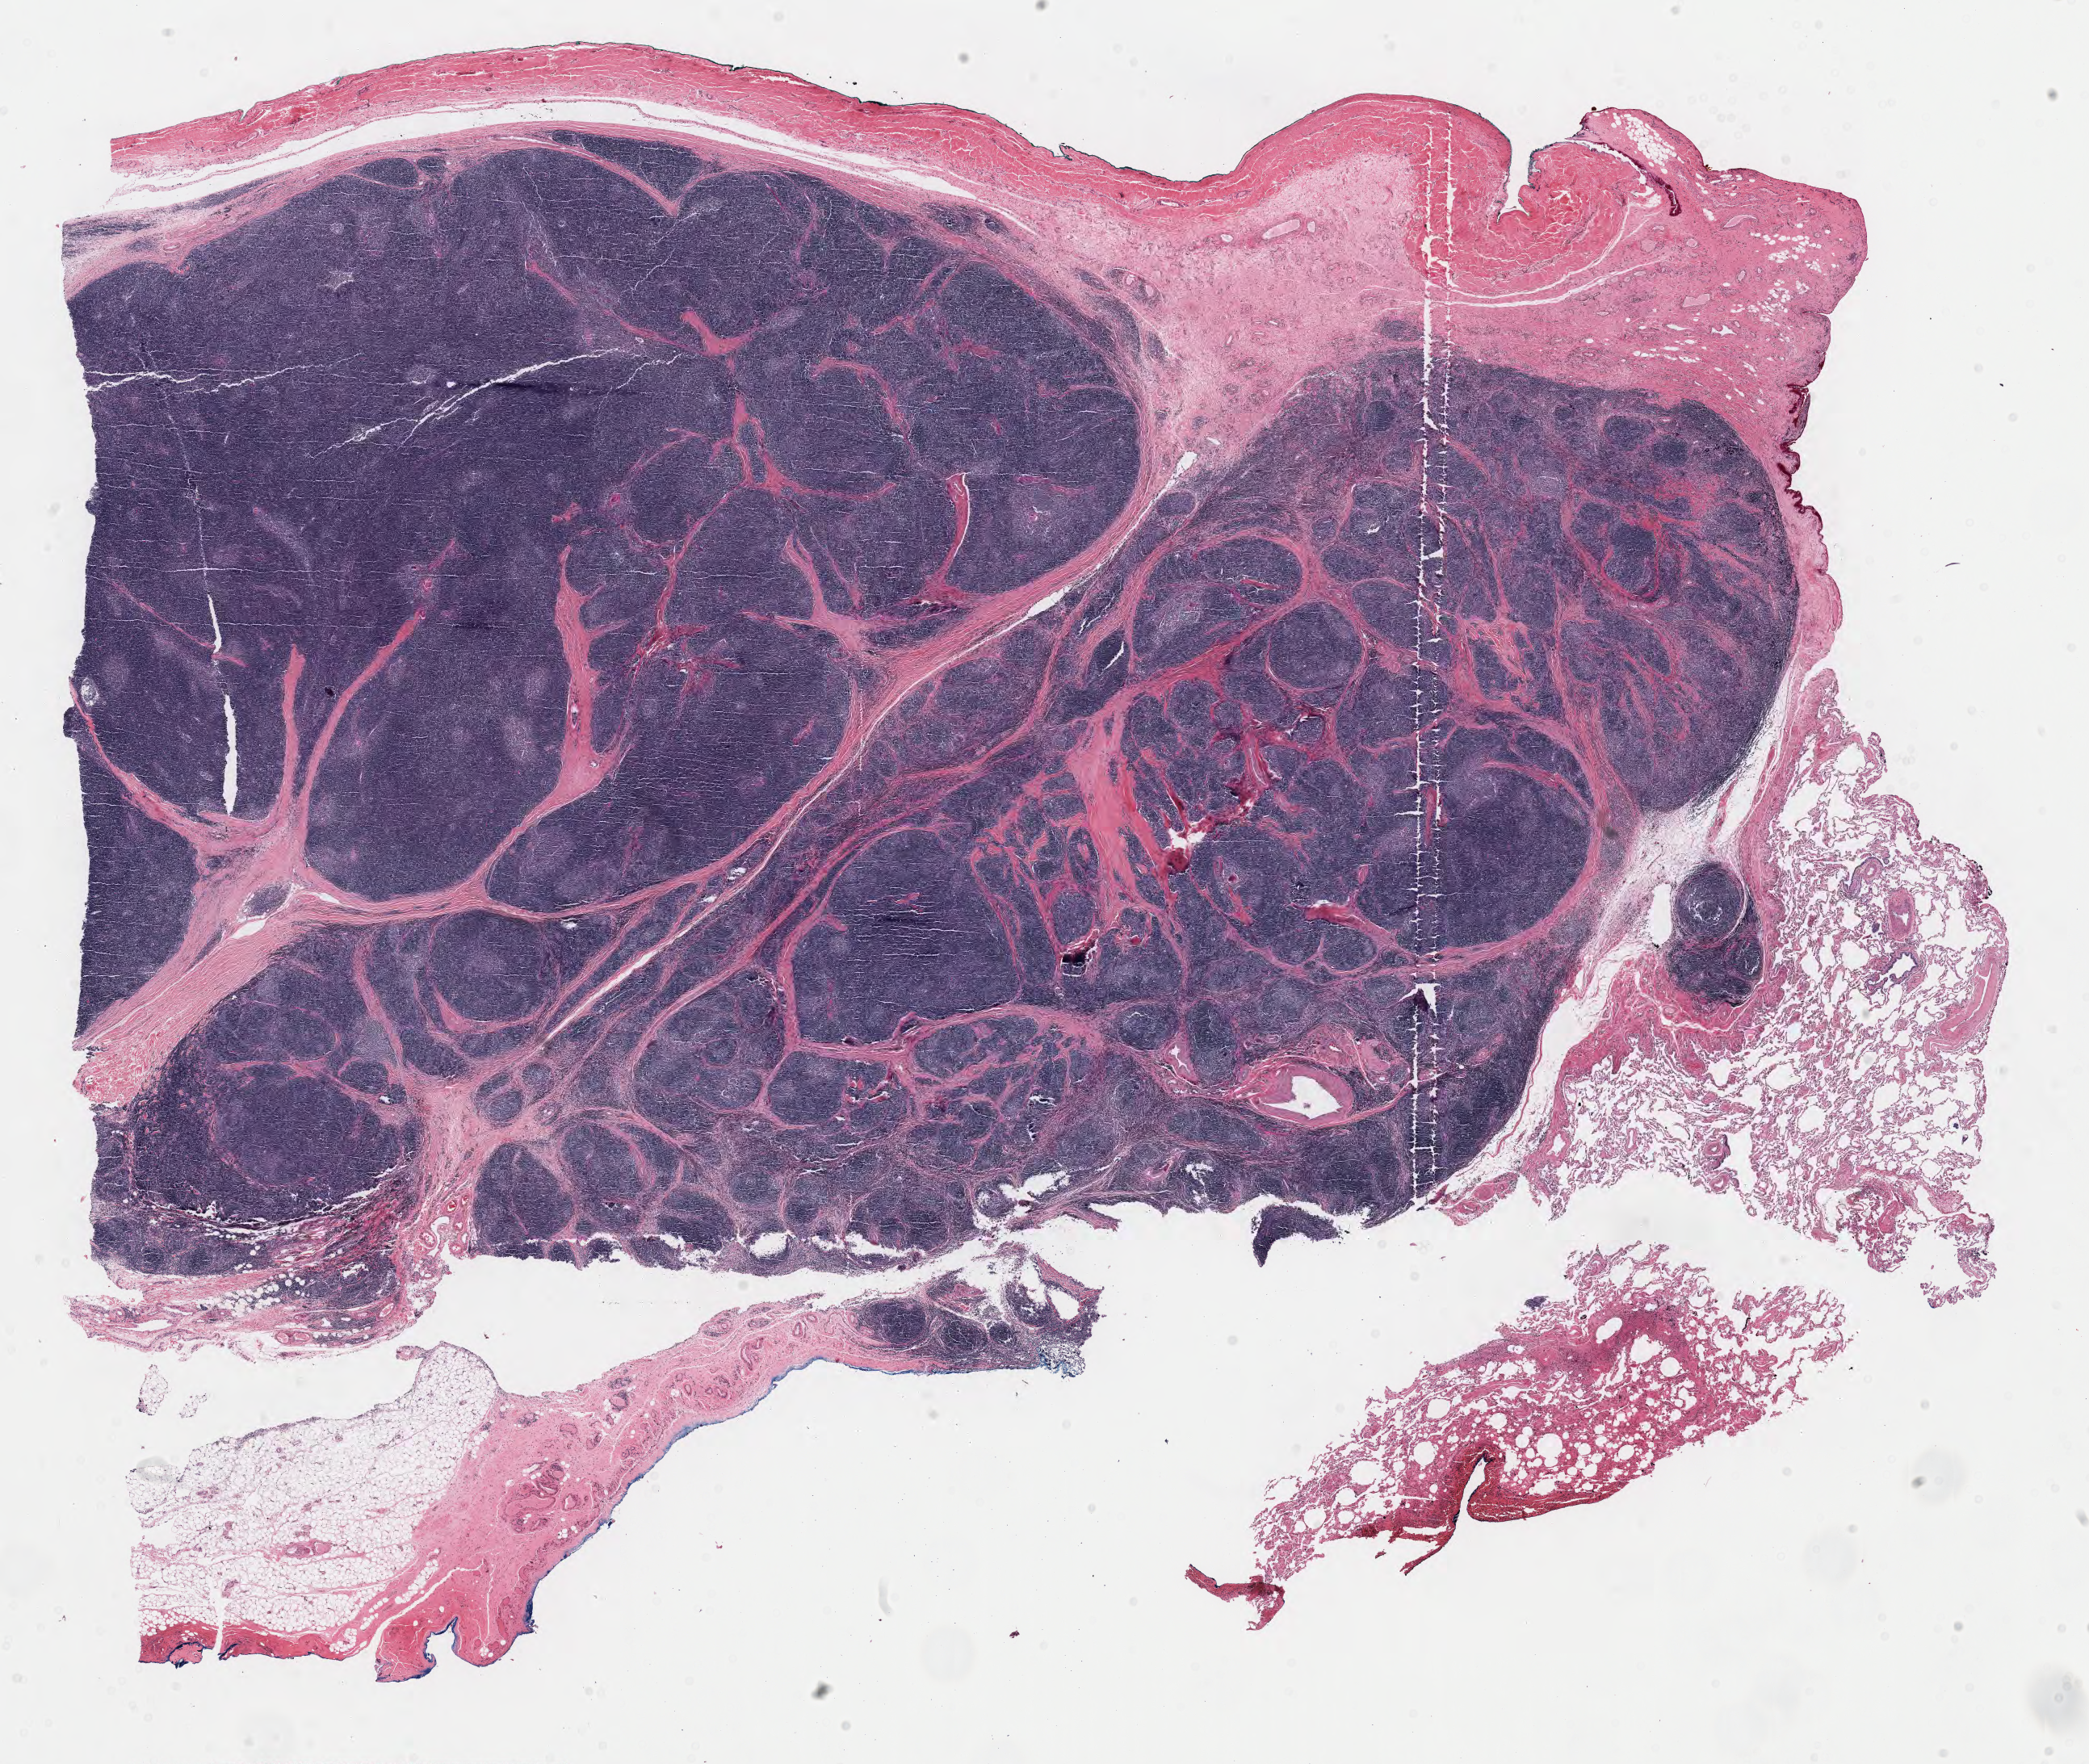
Digitized H&E-stained tissue section (whole slide) — low-resolution overview of the scanned area, about 20.5 x 17.3 mm (acquisition: 40x scan). FFPE section. Thymus, primary tumour sample. Female patient; age at initial diagnosis 57 years.
Pathologic diagnosis: Thymoma, type B1, NOS.